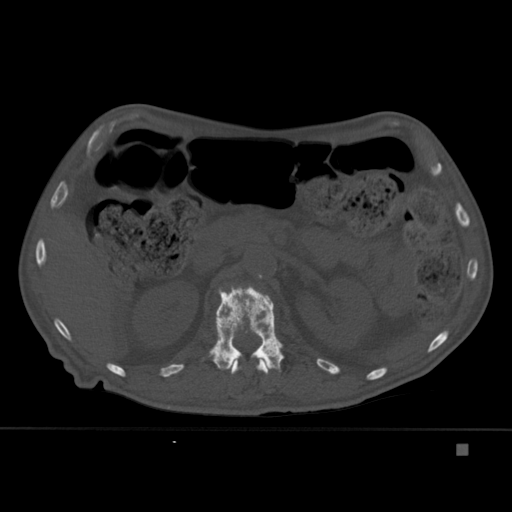
CT including the spine, one axial slice. Slice 185 of 451 in the series (ordered by position). Bone window (W 1800 / L 400 HU). 1.5 mm slice thickness. 512 × 512 image matrix, field of view 378 × 378 mm. Patient: male, 75 years. From the clinical record (not read from this slice): primary cancer: prostate.
Outlined on this slice (semi-automatically segmented with operator editing):
- L1 vertebra: bounding box <203,285,285,372> (left, top, right, bottom; pixels)
- T12 vertebra: <231,358,268,375>